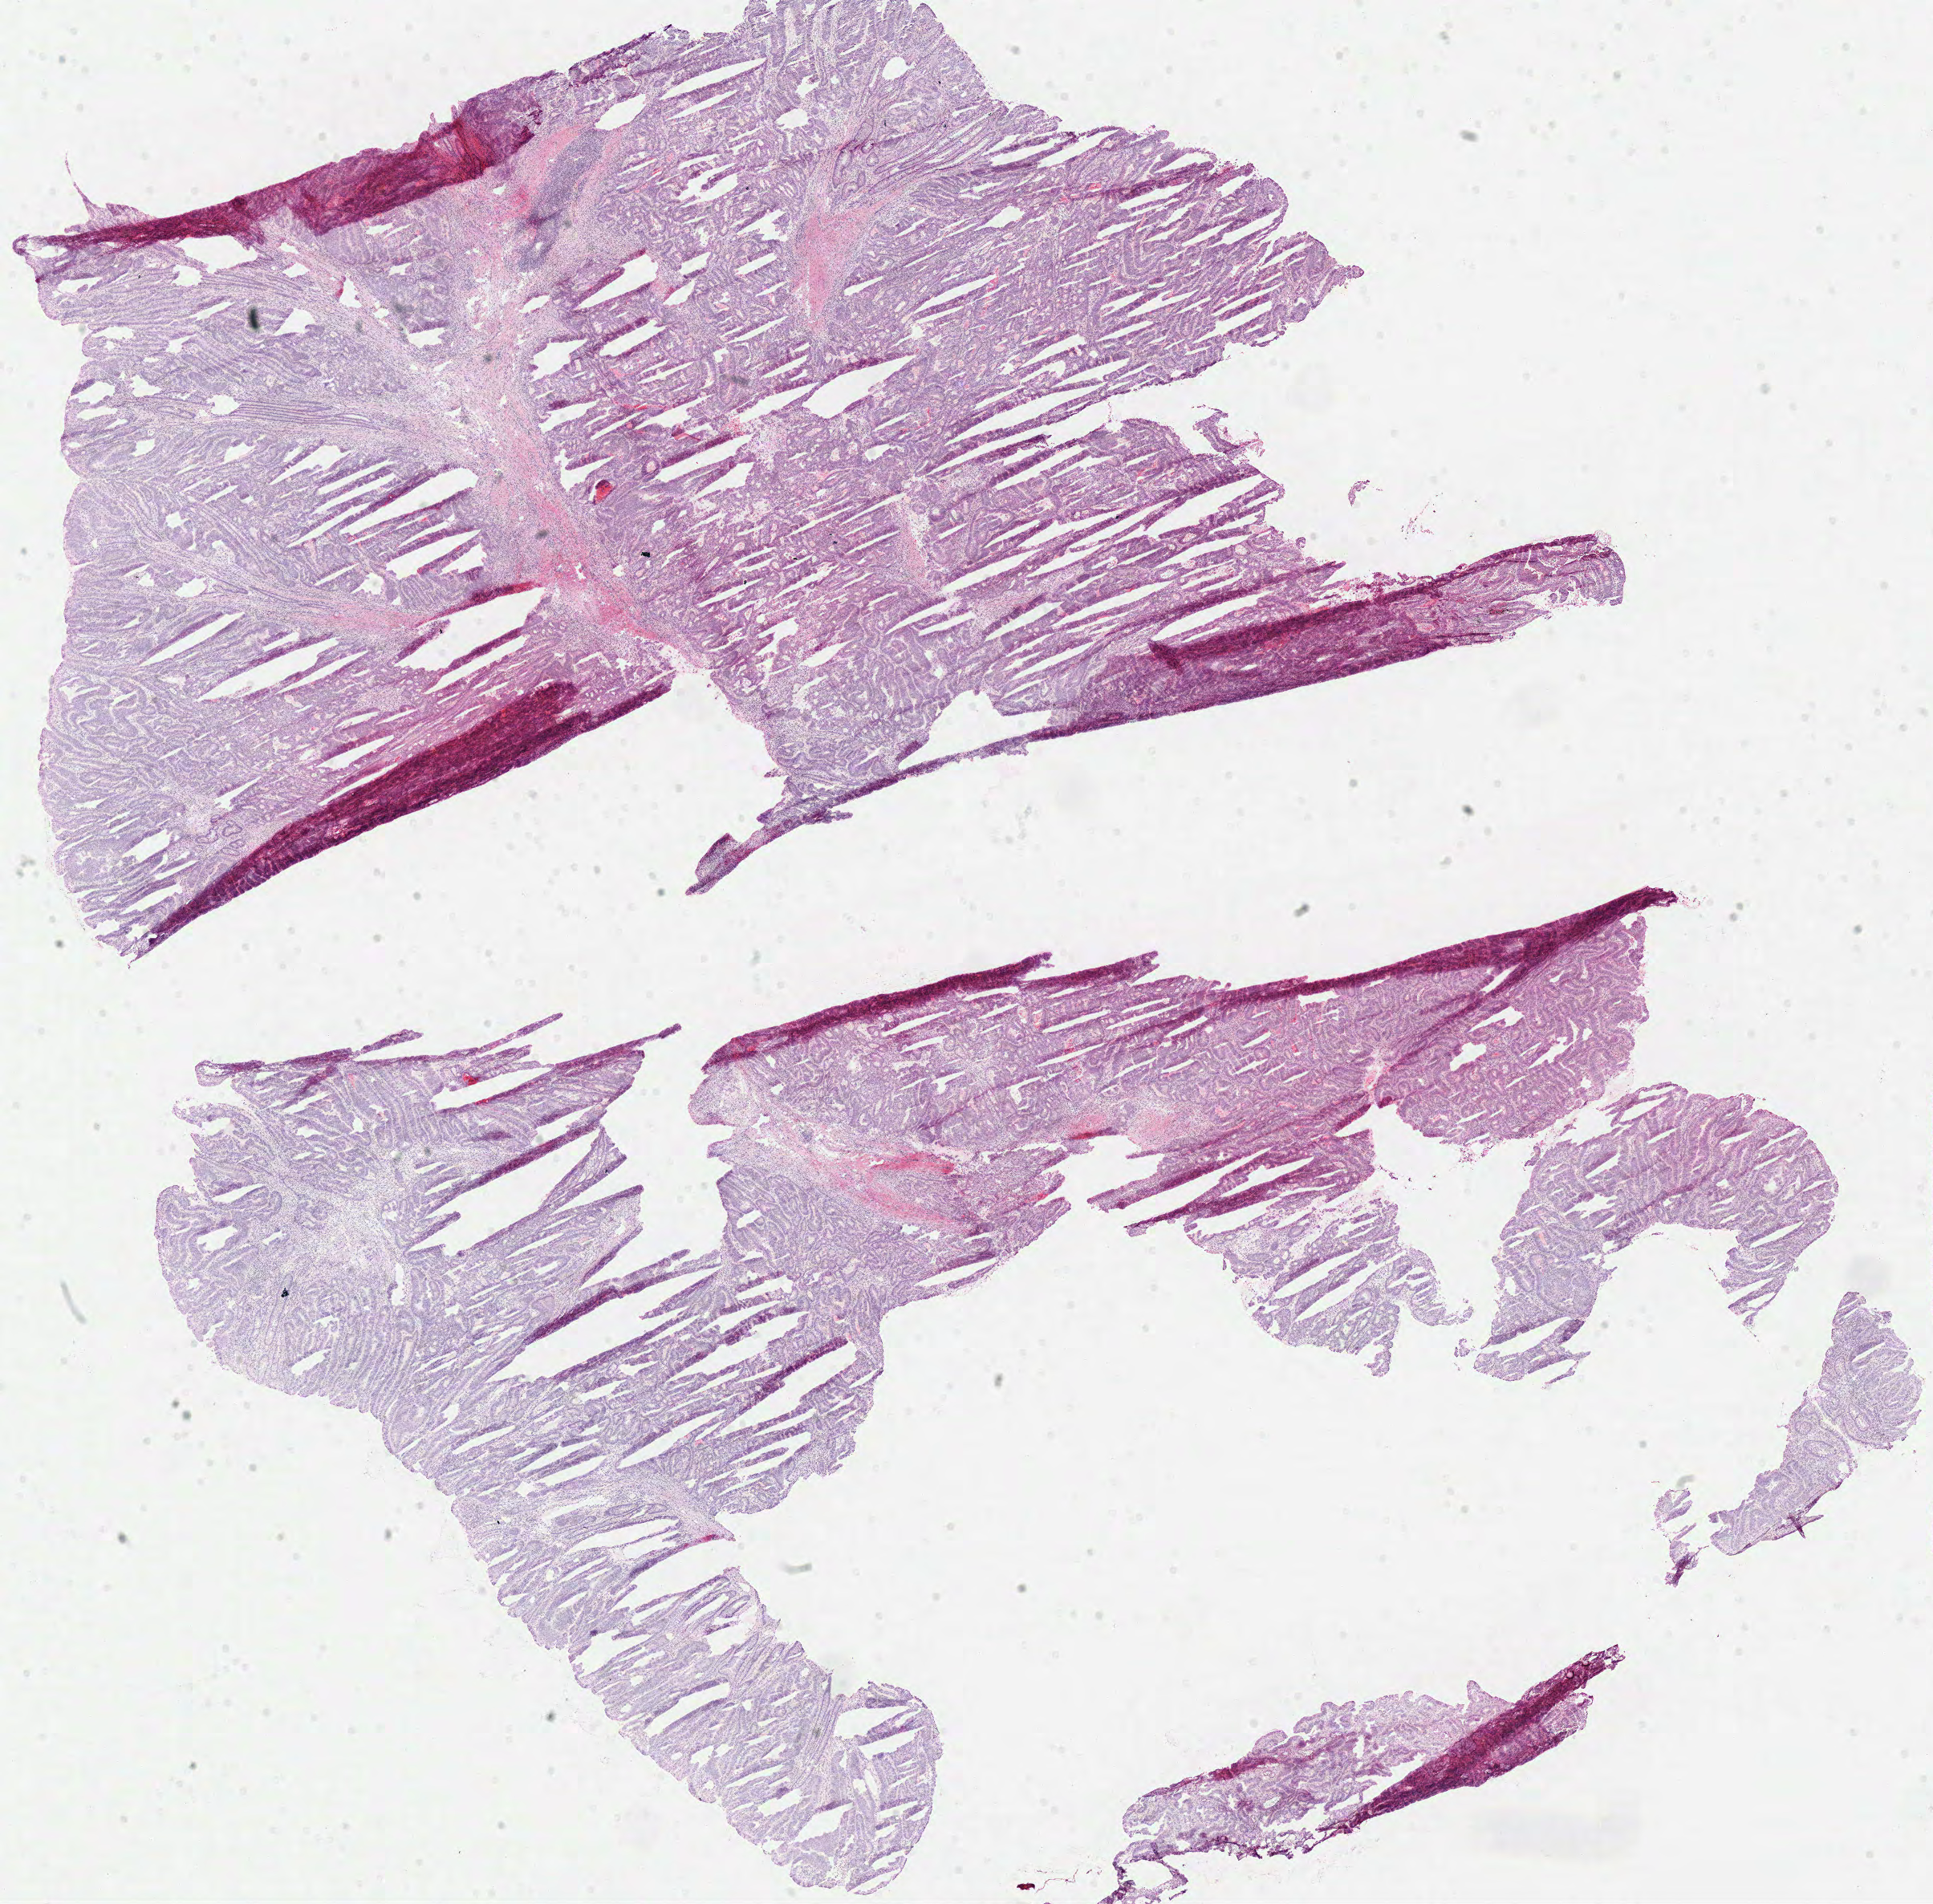
H&E whole-slide image — low-resolution overview of the scanned area, about 19.0 x 18.7 mm (slide scanned at 40x); frozen section; colon, primary tumour sample. Female patient; age at initial diagnosis 36 years. Pathologist review of this section (percent, as recorded): tumour cells 79%, tumour nuclei 80%, normal cells 3%, stromal cells 10%, necrosis 8%.
Lymph nodes positive (case pathology): 0 of 31 examined. AJCC pathologic stage: I (7th edition). Diagnosis: Adenocarcinoma, NOS.